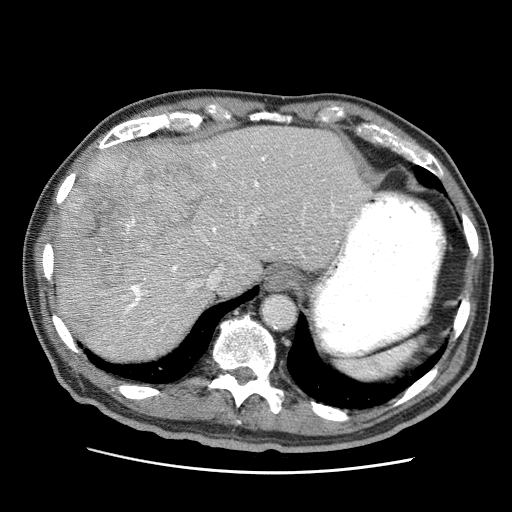
Contrast-enhanced abdominal CT (liver protocol), one axial slice; slice 50 of 75 in the series (ordered by position); reconstruction kernel STANDARD; 120 kVp; soft-tissue window (W 400 / L 40 HU); 512 × 512 image matrix, field of view 360 × 360 mm. From the clinical record (not read from this slice): diagnosis: hepatocellular carcinoma (patient treated with transarterial chemoembolisation; whether this scan precedes or follows treatment is not stated here); TNM stage (as recorded): Stage-IIIA; Child-Pugh class: A; tumour differentiation: well differentiated.
Structures marked on this image (semi-automatic segmentation, software-assisted and operator-edited):
- abdominal aorta: bounding box <263,295,296,329> (left, top, right, bottom; pixels)
- liver parenchyma outside the tumour (the mass and vessels are separate outlines, so this box may not span the whole liver): <54,126,370,360>
- mass: <59,145,213,342>
- liver vessels: <108,152,338,349>